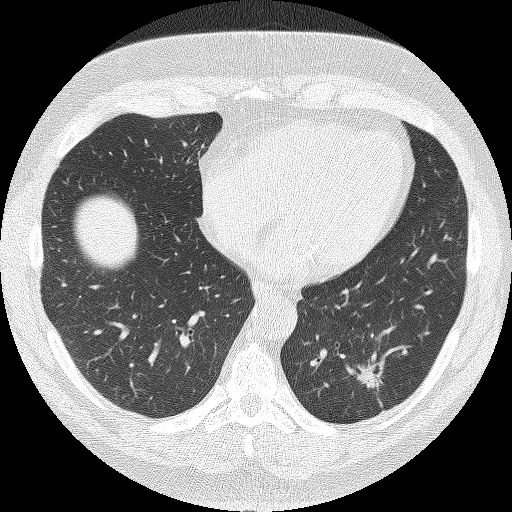
Axial slice from a low-dose chest CT screening exam, baseline screening round, lung window (W 1500 / L -600 HU), 2 mm slice thickness, slice 95 of 140 in the series. Male, age 62 years at enrolment. Current smoker at enrolment.
Expert reader's lesion annotation, bounding box [x1, y1, x2, y2] px = [348, 354, 404, 407]. The screening reader recorded 2 non-calcified nodules or masses ≥4 mm on this exam (left lower lobe, right upper lobe); which of them this box marks is not recorded. Lung cancer was diagnosed 90 days after this screen: adenocarcinoma, NOS, left lower lobe, moderately differentiated (G2), stage IA (AJCC 6th edition), 30 mm at pathology.